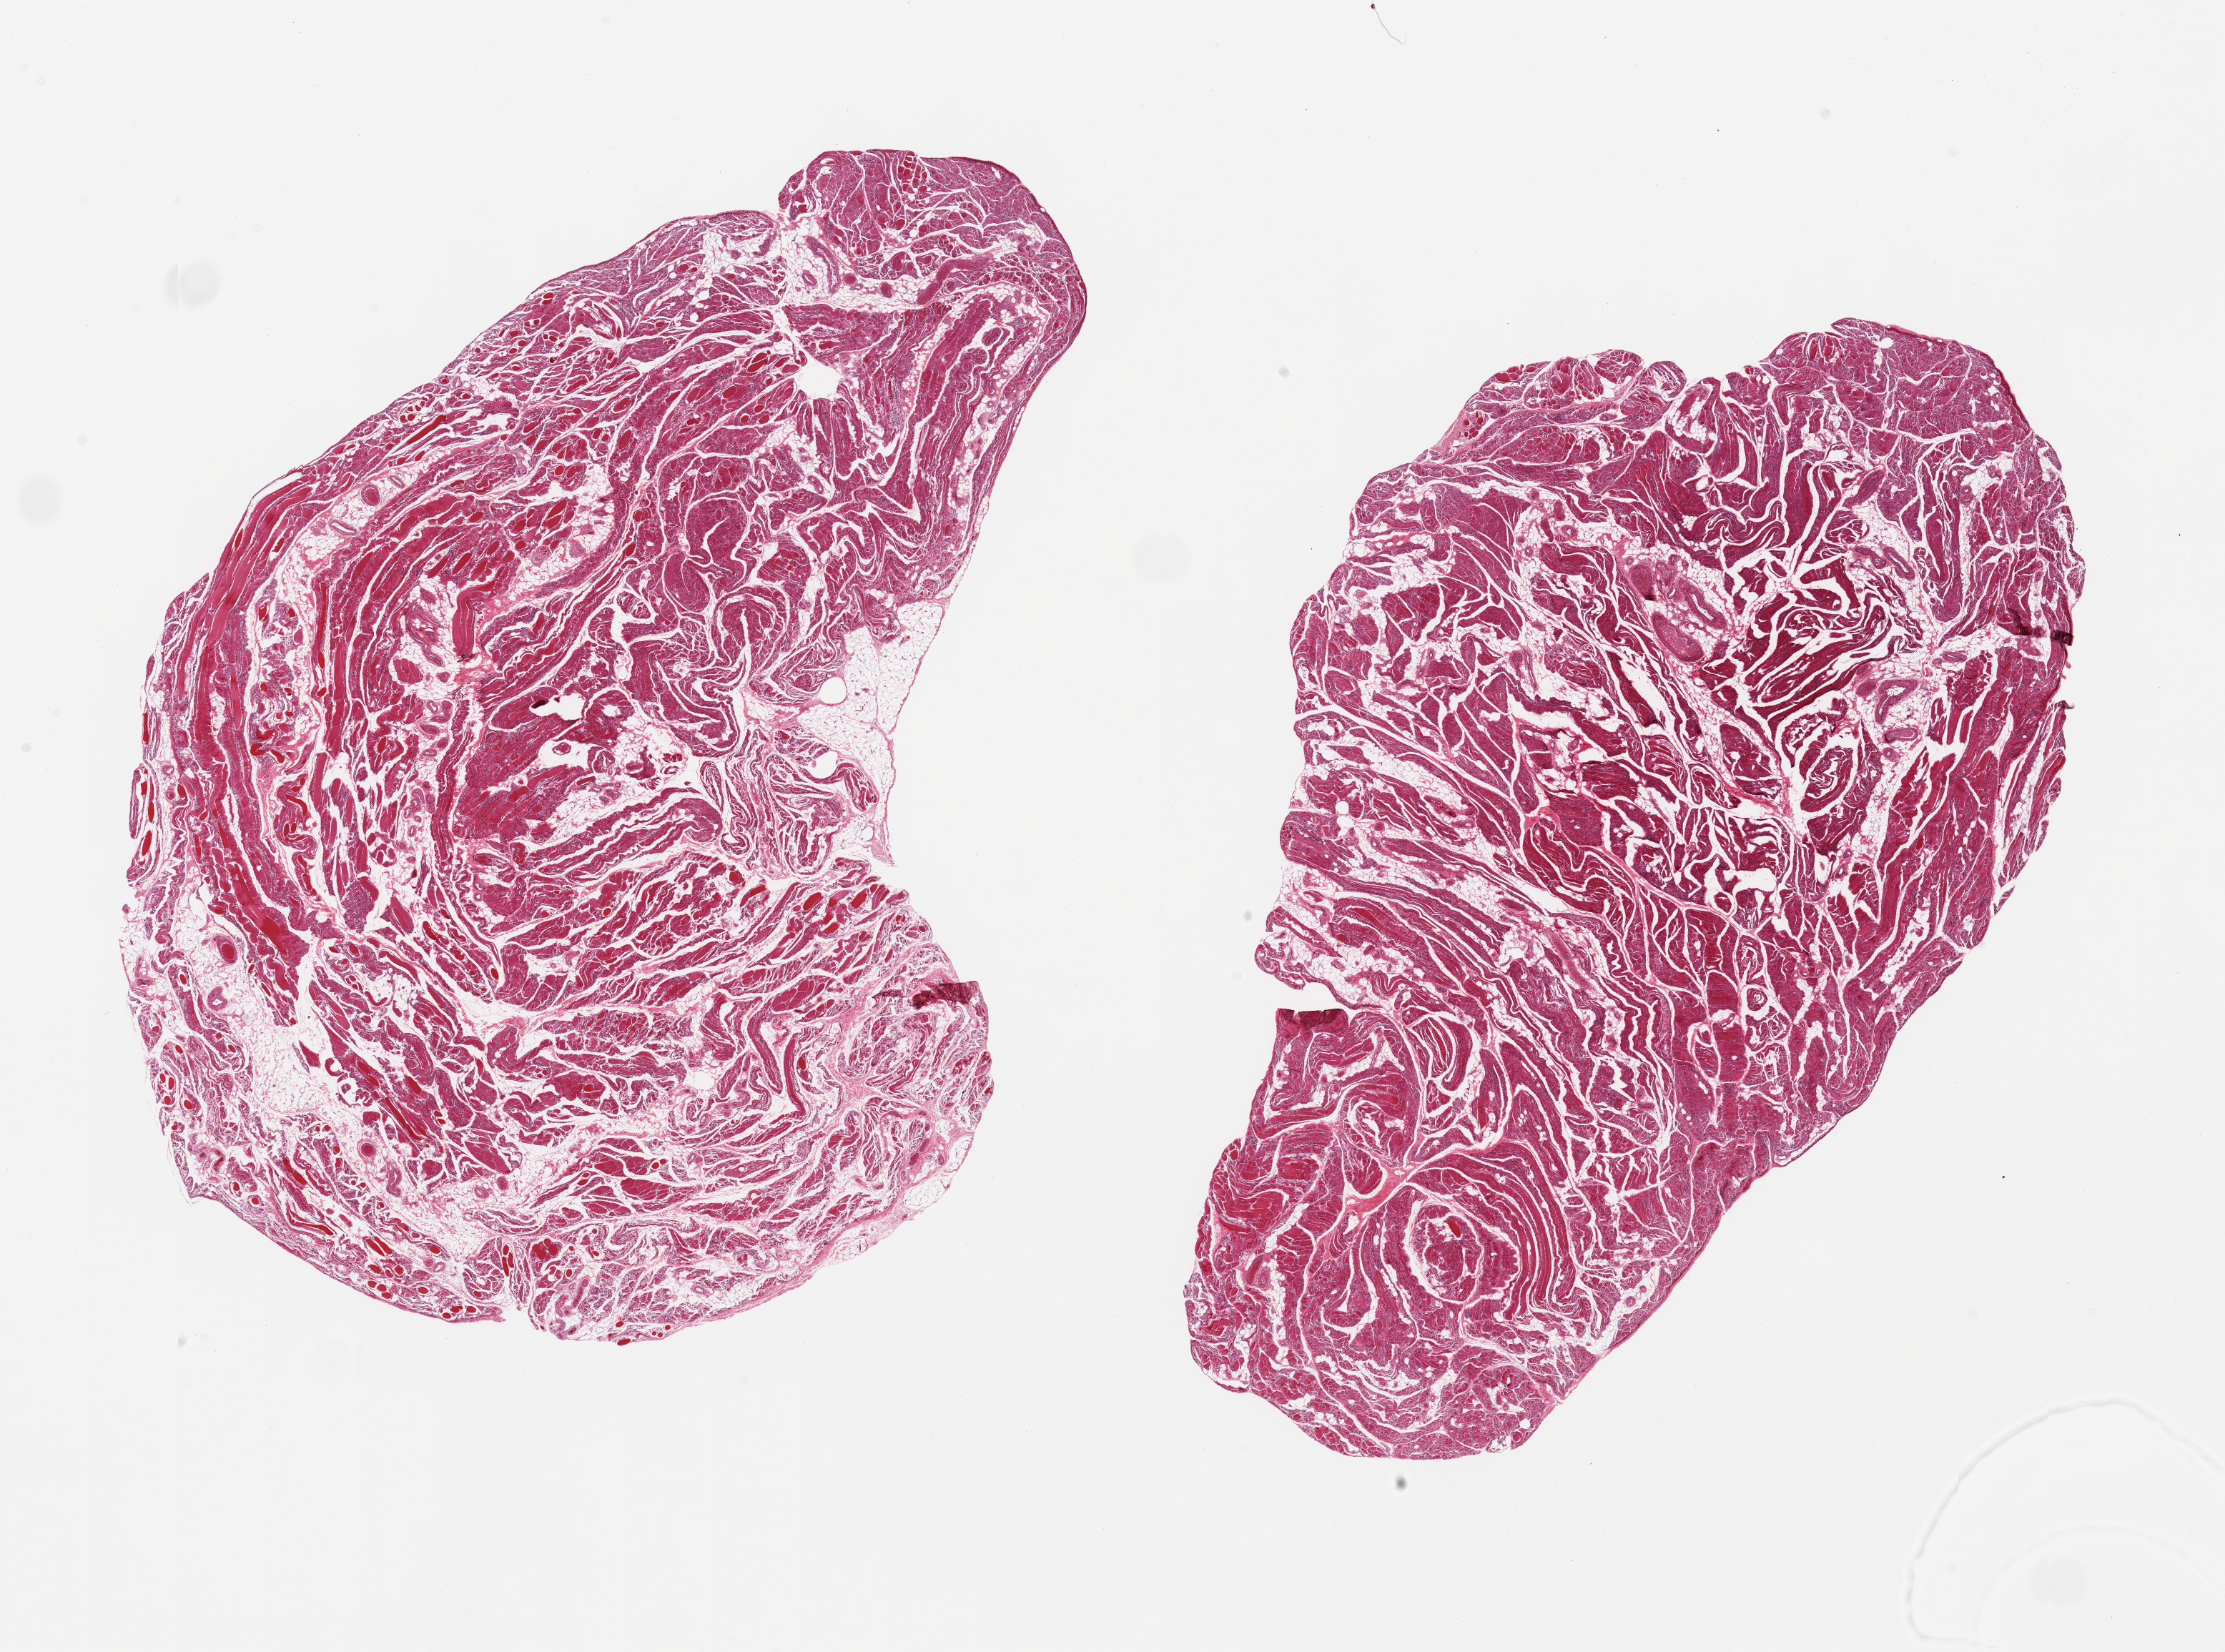
Whole-slide image, hematoxylin and eosin (H&E) stain — whole scanned area (about 24.6 x 18.3 mm, acquisition: 20x scan) shown as a low-resolution overview. PAXgene-fixed, paraffin-embedded tissue. Target tissue: skeletal muscle. Donor tissue sample. Donor sex: male.
Review note (as recorded): 2 pieces, ~50% interstitial fat/edema, evidence of atrophy.